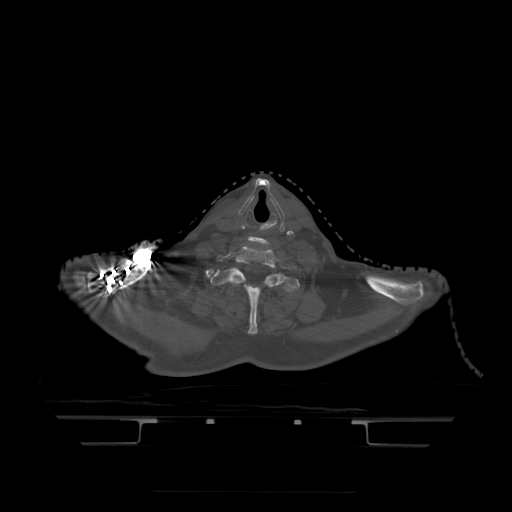
CT including the spine, one axial slice. Bone window (W 1800 / L 400 HU). 1.25 mm slice thickness. 512 × 512 image matrix, field of view 436 × 436 mm. Patient age 68 years. Case-level facts recorded for this patient, not image findings: primary cancer: urothelial.
Annotated regions visible in this slice (semi-automatic segmentation, software-assisted and operator-edited):
- T1 vertebra: box from (x=211, y=269) to (x=301, y=335) px